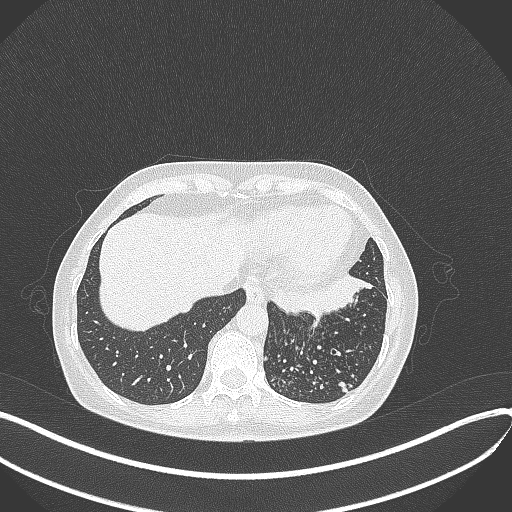
Chest CT, one axial slice; slice 96 of 429 in the series (ordered by position); 100 kVp; lung window (W 1500 / L -600 HU); 512 × 512 image matrix, field of view 400 × 400 mm. Patient: female, 63 years. From the clinical record (not read from this slice): clinical TNM (as recorded): T1b N0 M0; histopathological grade: G2-3.
Structures marked on this image (rectangle marked by the reading radiologist):
- lung tumour (recorded histology: adenocarcinoma): bounding box [x1, y1, x2, y2] px = [278, 271, 371, 315]